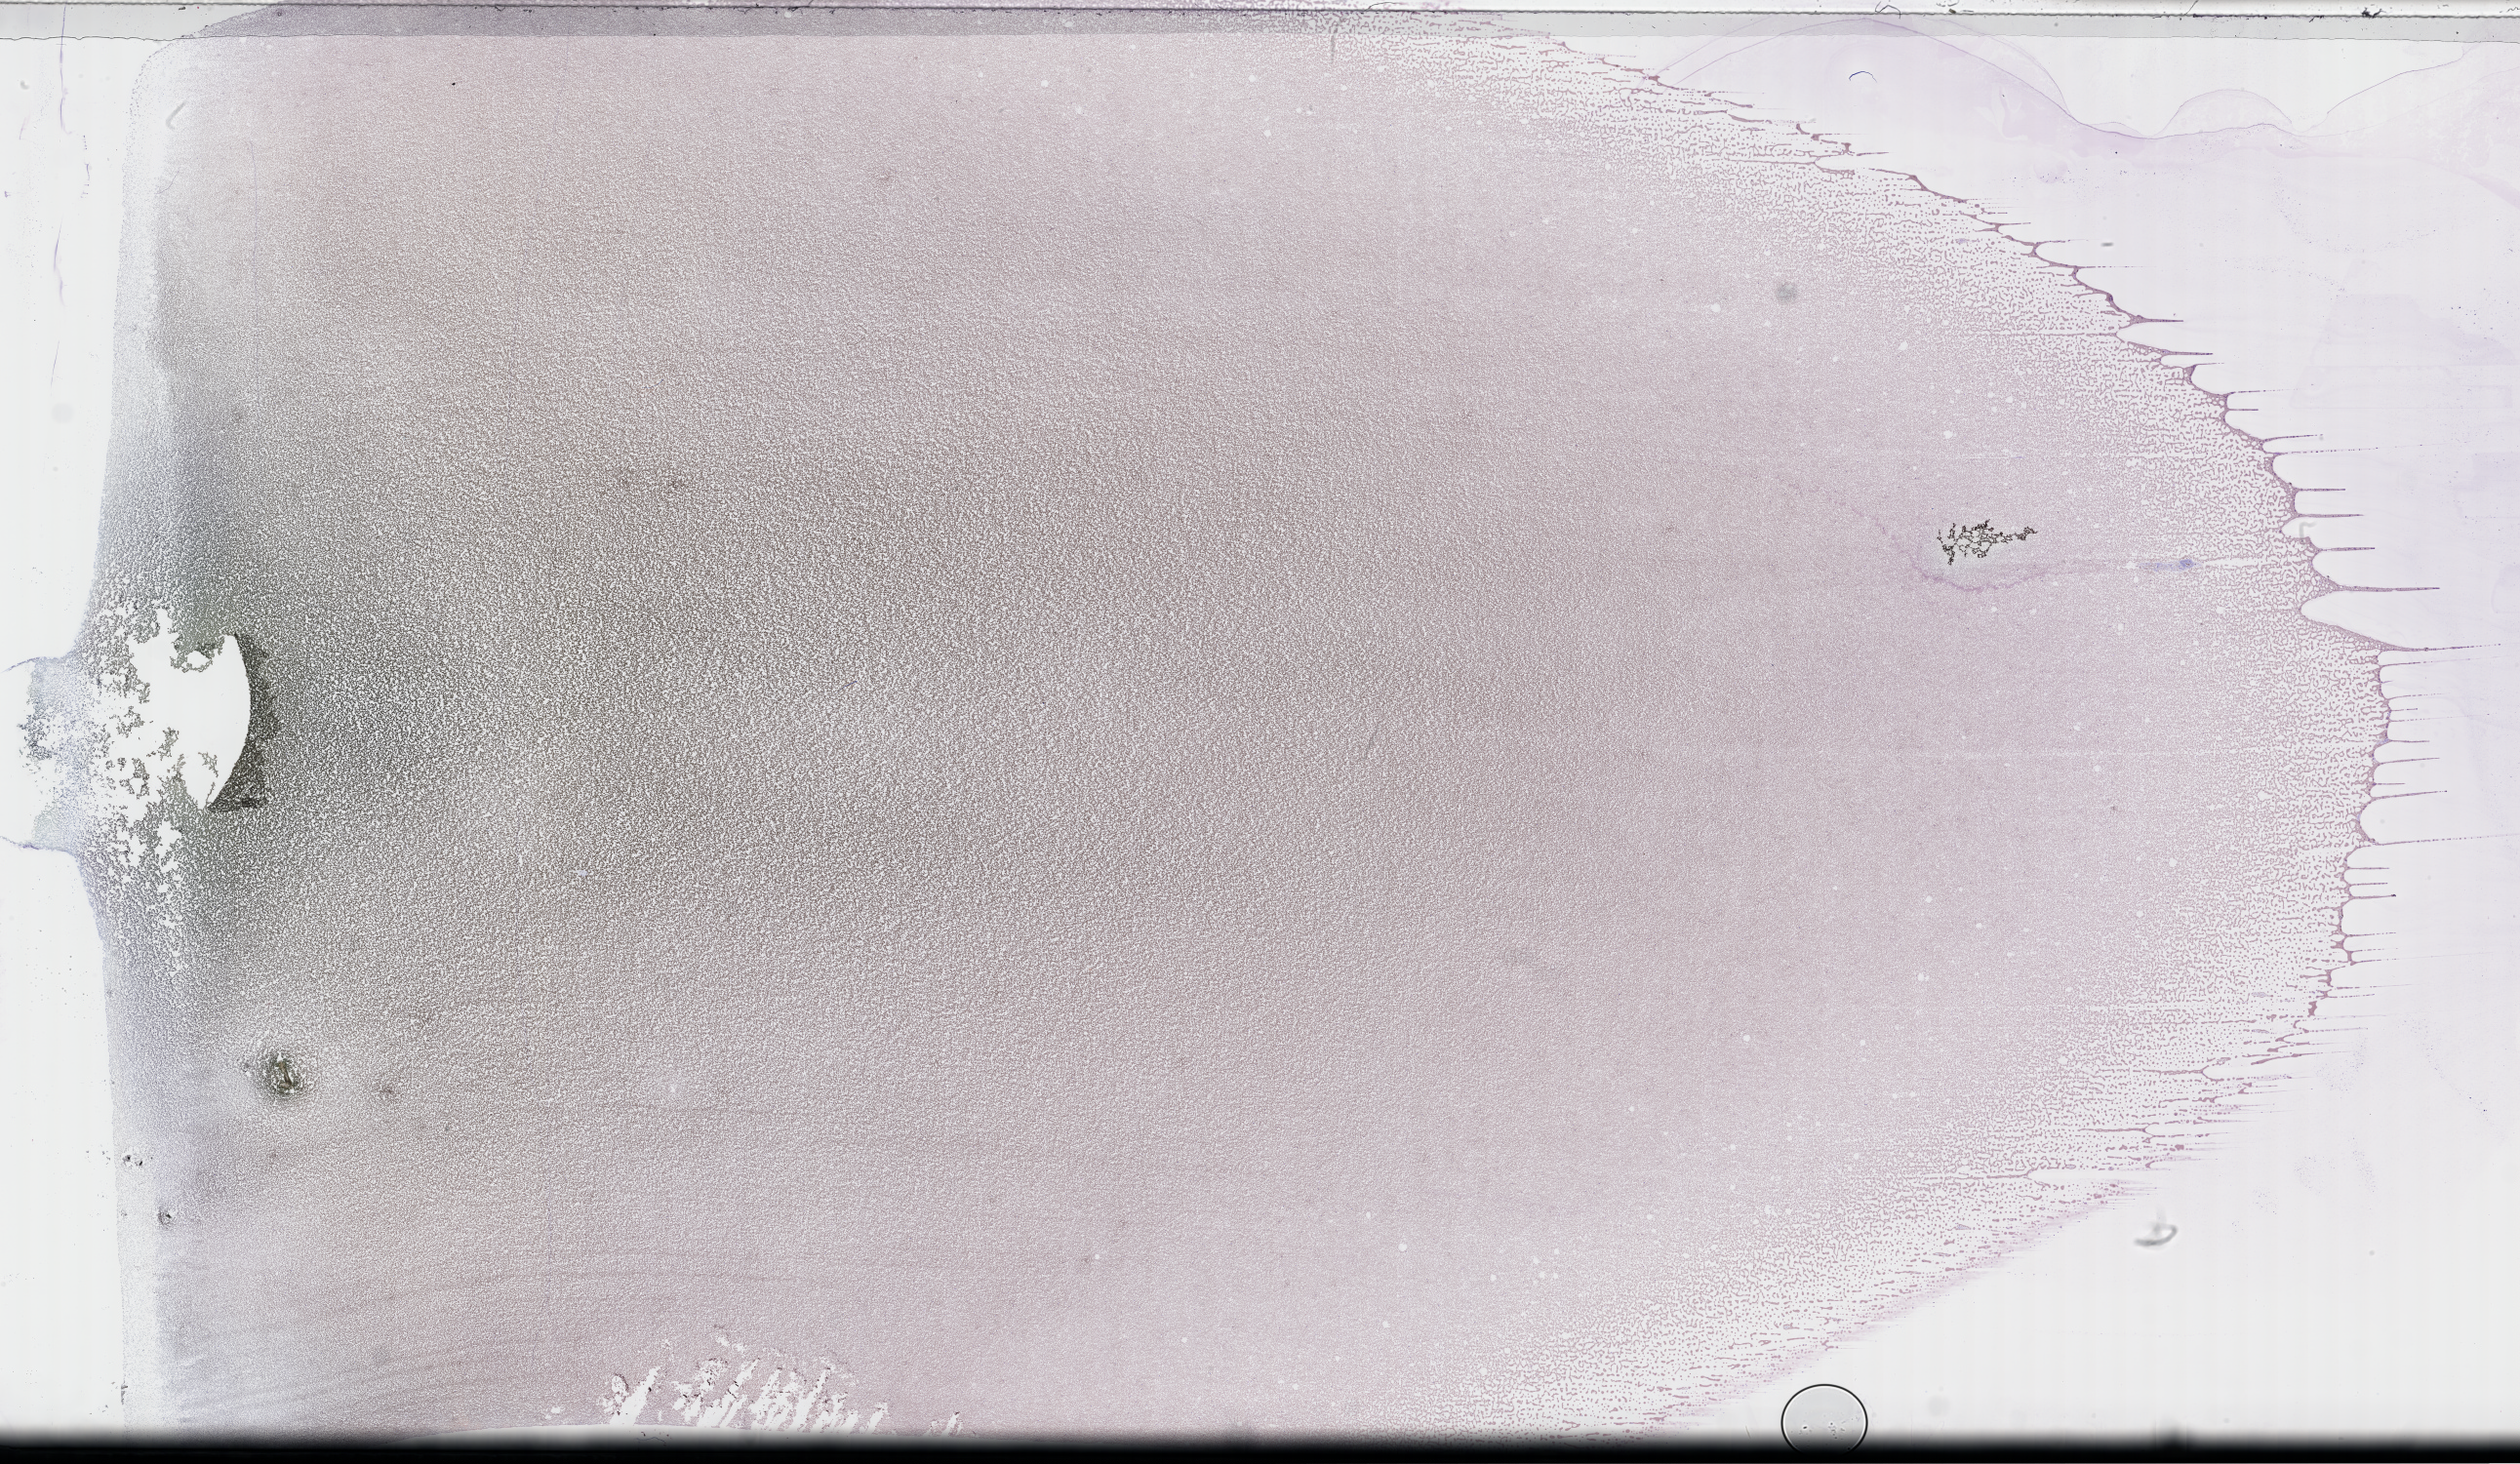
Wright-Giemsa-stained whole blood smear, whole-slide image — whole scanned area (about 41.7 x 24.2 mm) shown as a low-resolution overview. EDTA-anticoagulated smear. Patient: male.
From a patient with: Plasma Cell Myeloma.